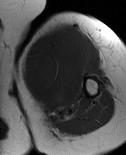
MRI of an extremity soft-tissue mass, one axial slice; slice 51 of 86 in the series (ordered by position); MR volume resampled by the dataset authors to the PET/CT grid (not the native acquisition matrix); 3.27 mm slice thickness; 126 × 155 image matrix, field of view 123 × 151 mm. Female patient. From the clinical record (not read from this slice): histological type: pleiomorphic leiomyosarcoma; grade: high; site of the primary tumour: left biceps.
Structures marked on this image (expert contour drawn on MRI and transferred to this co-registered scan by the dataset authors):
- gross tumour volume including surrounding oedema: box from (x=22, y=24) to (x=94, y=118) px
- gross tumour volume (mass): (x=22, y=26)–(x=89, y=112)